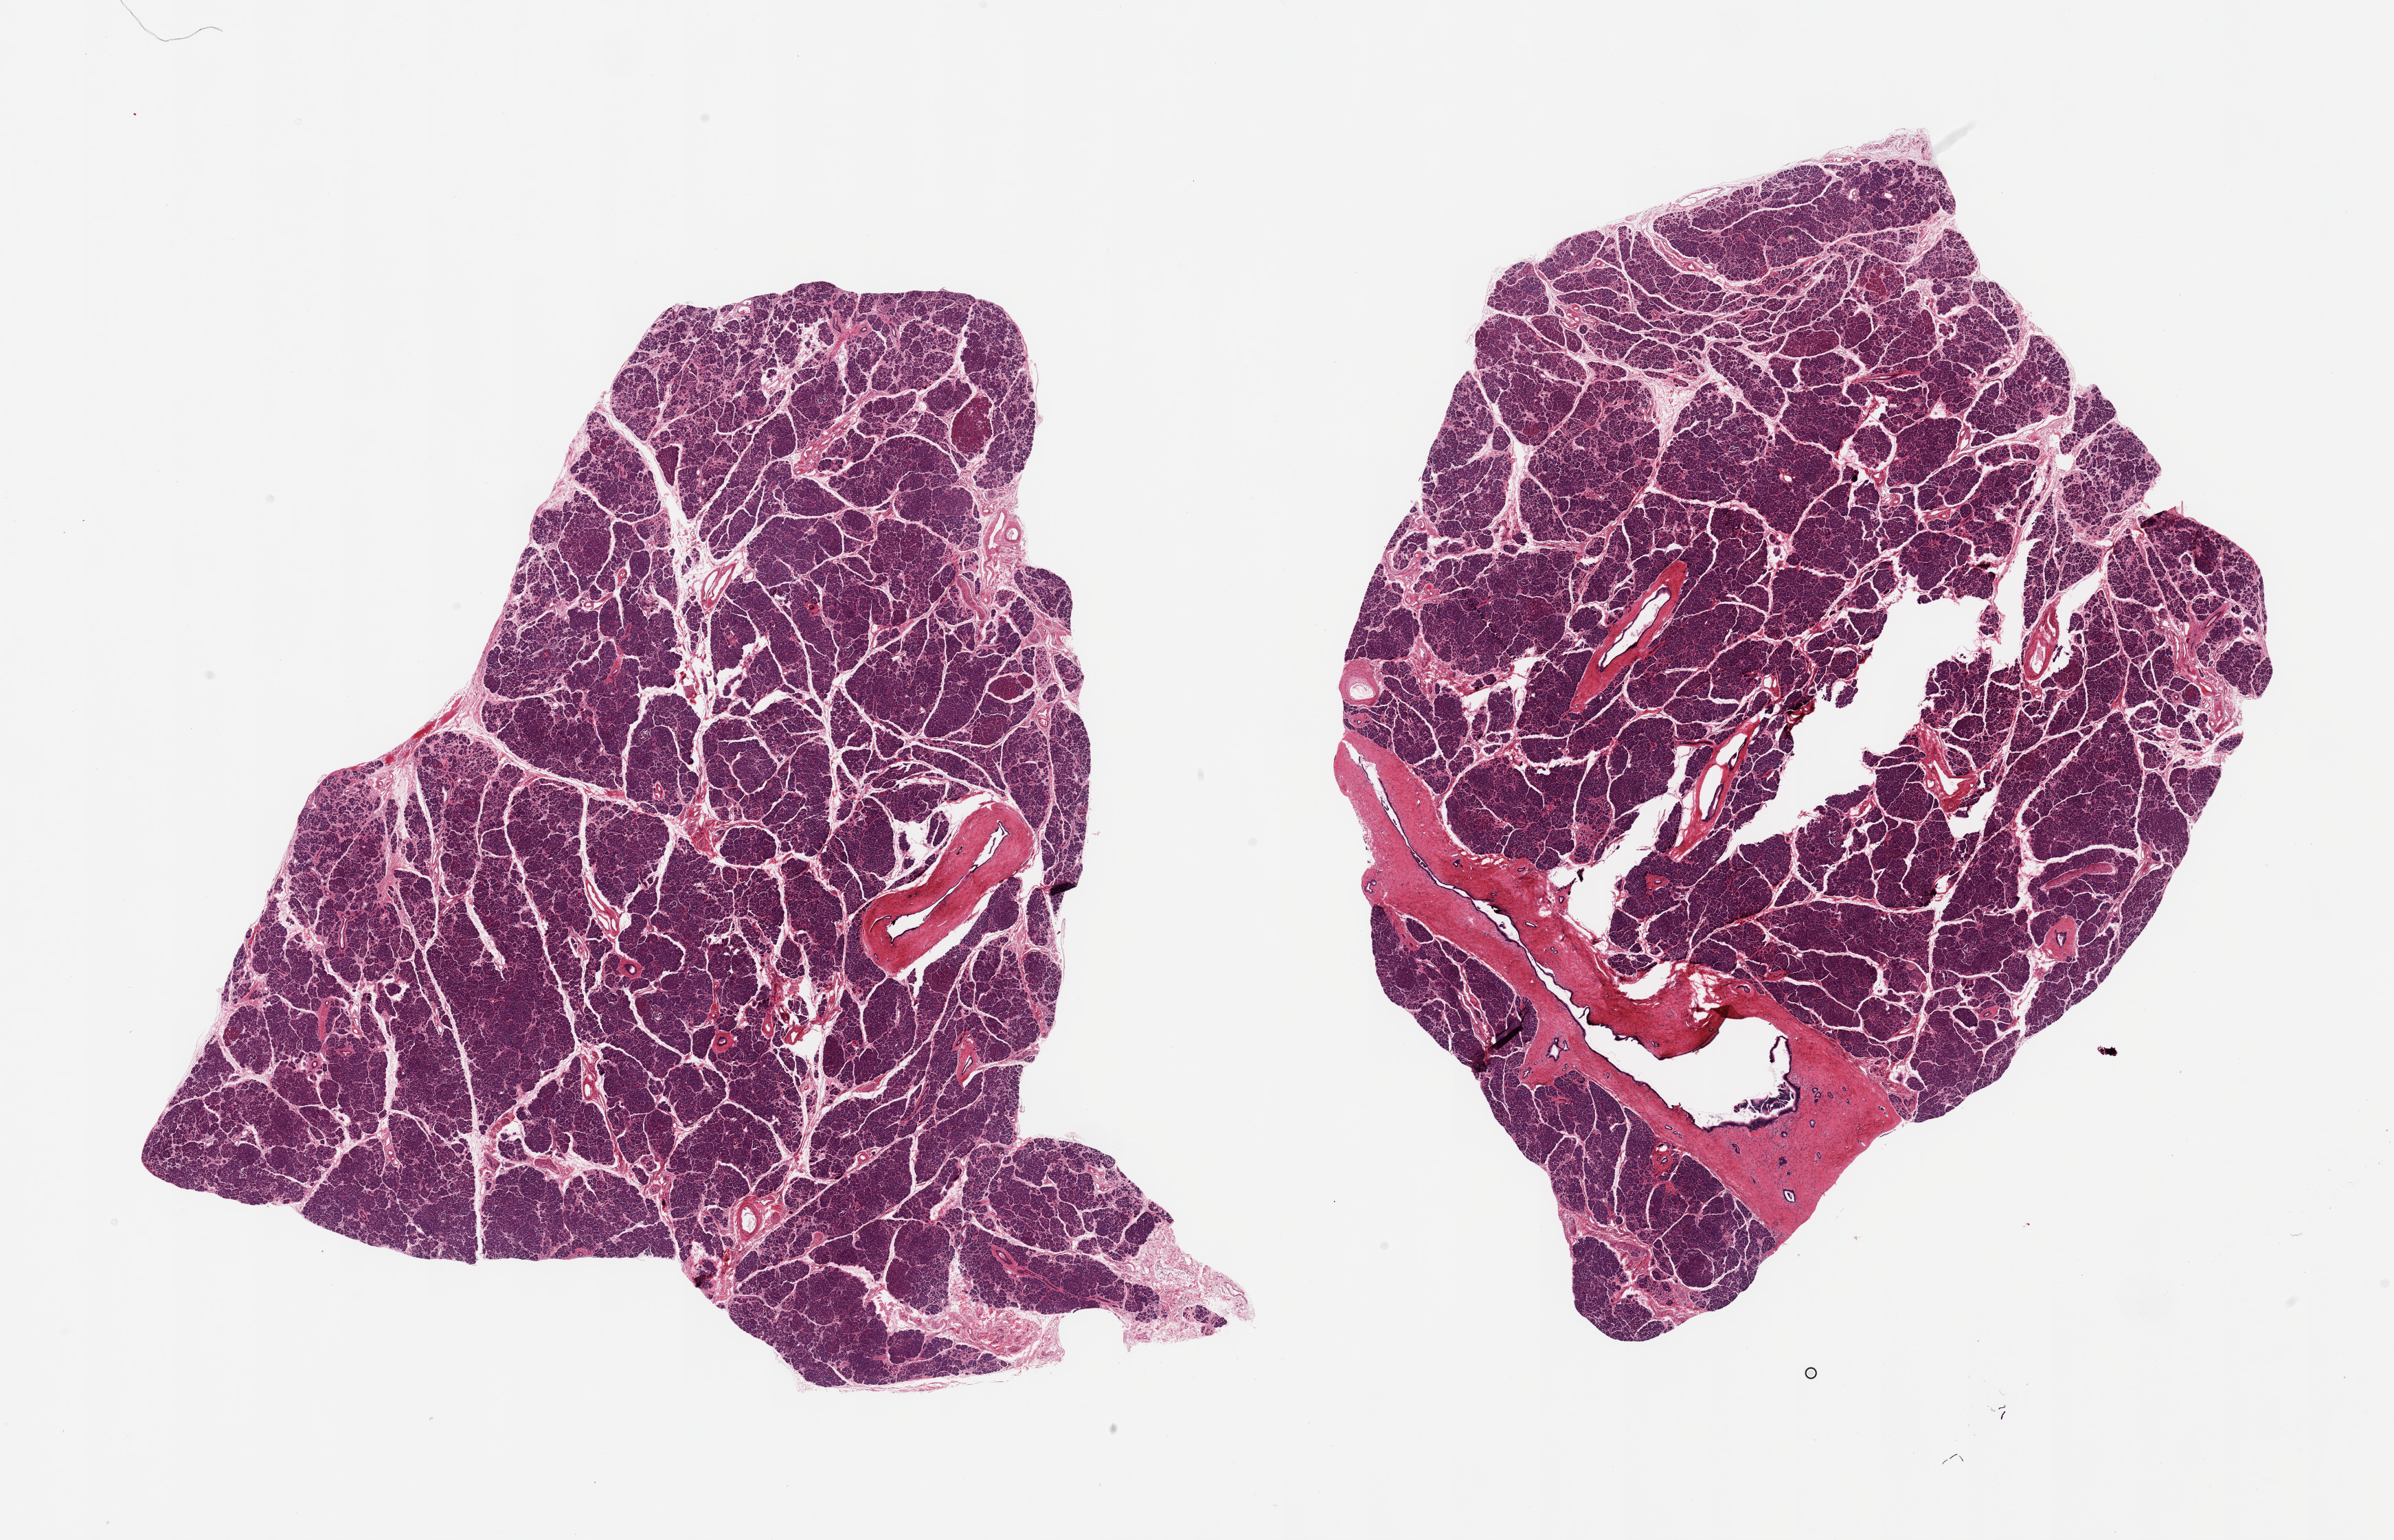
Digitized H&E-stained section — whole scanned area (about 27.6 x 17.7 mm) shown as a low-resolution overview, PAXgene-fixed, paraffin-embedded tissue, target tissue: pancreas, donor tissue sample.
Pathologist's review note for this sample: 2 pieces, reasonably well preserved, Islets visible but rare.